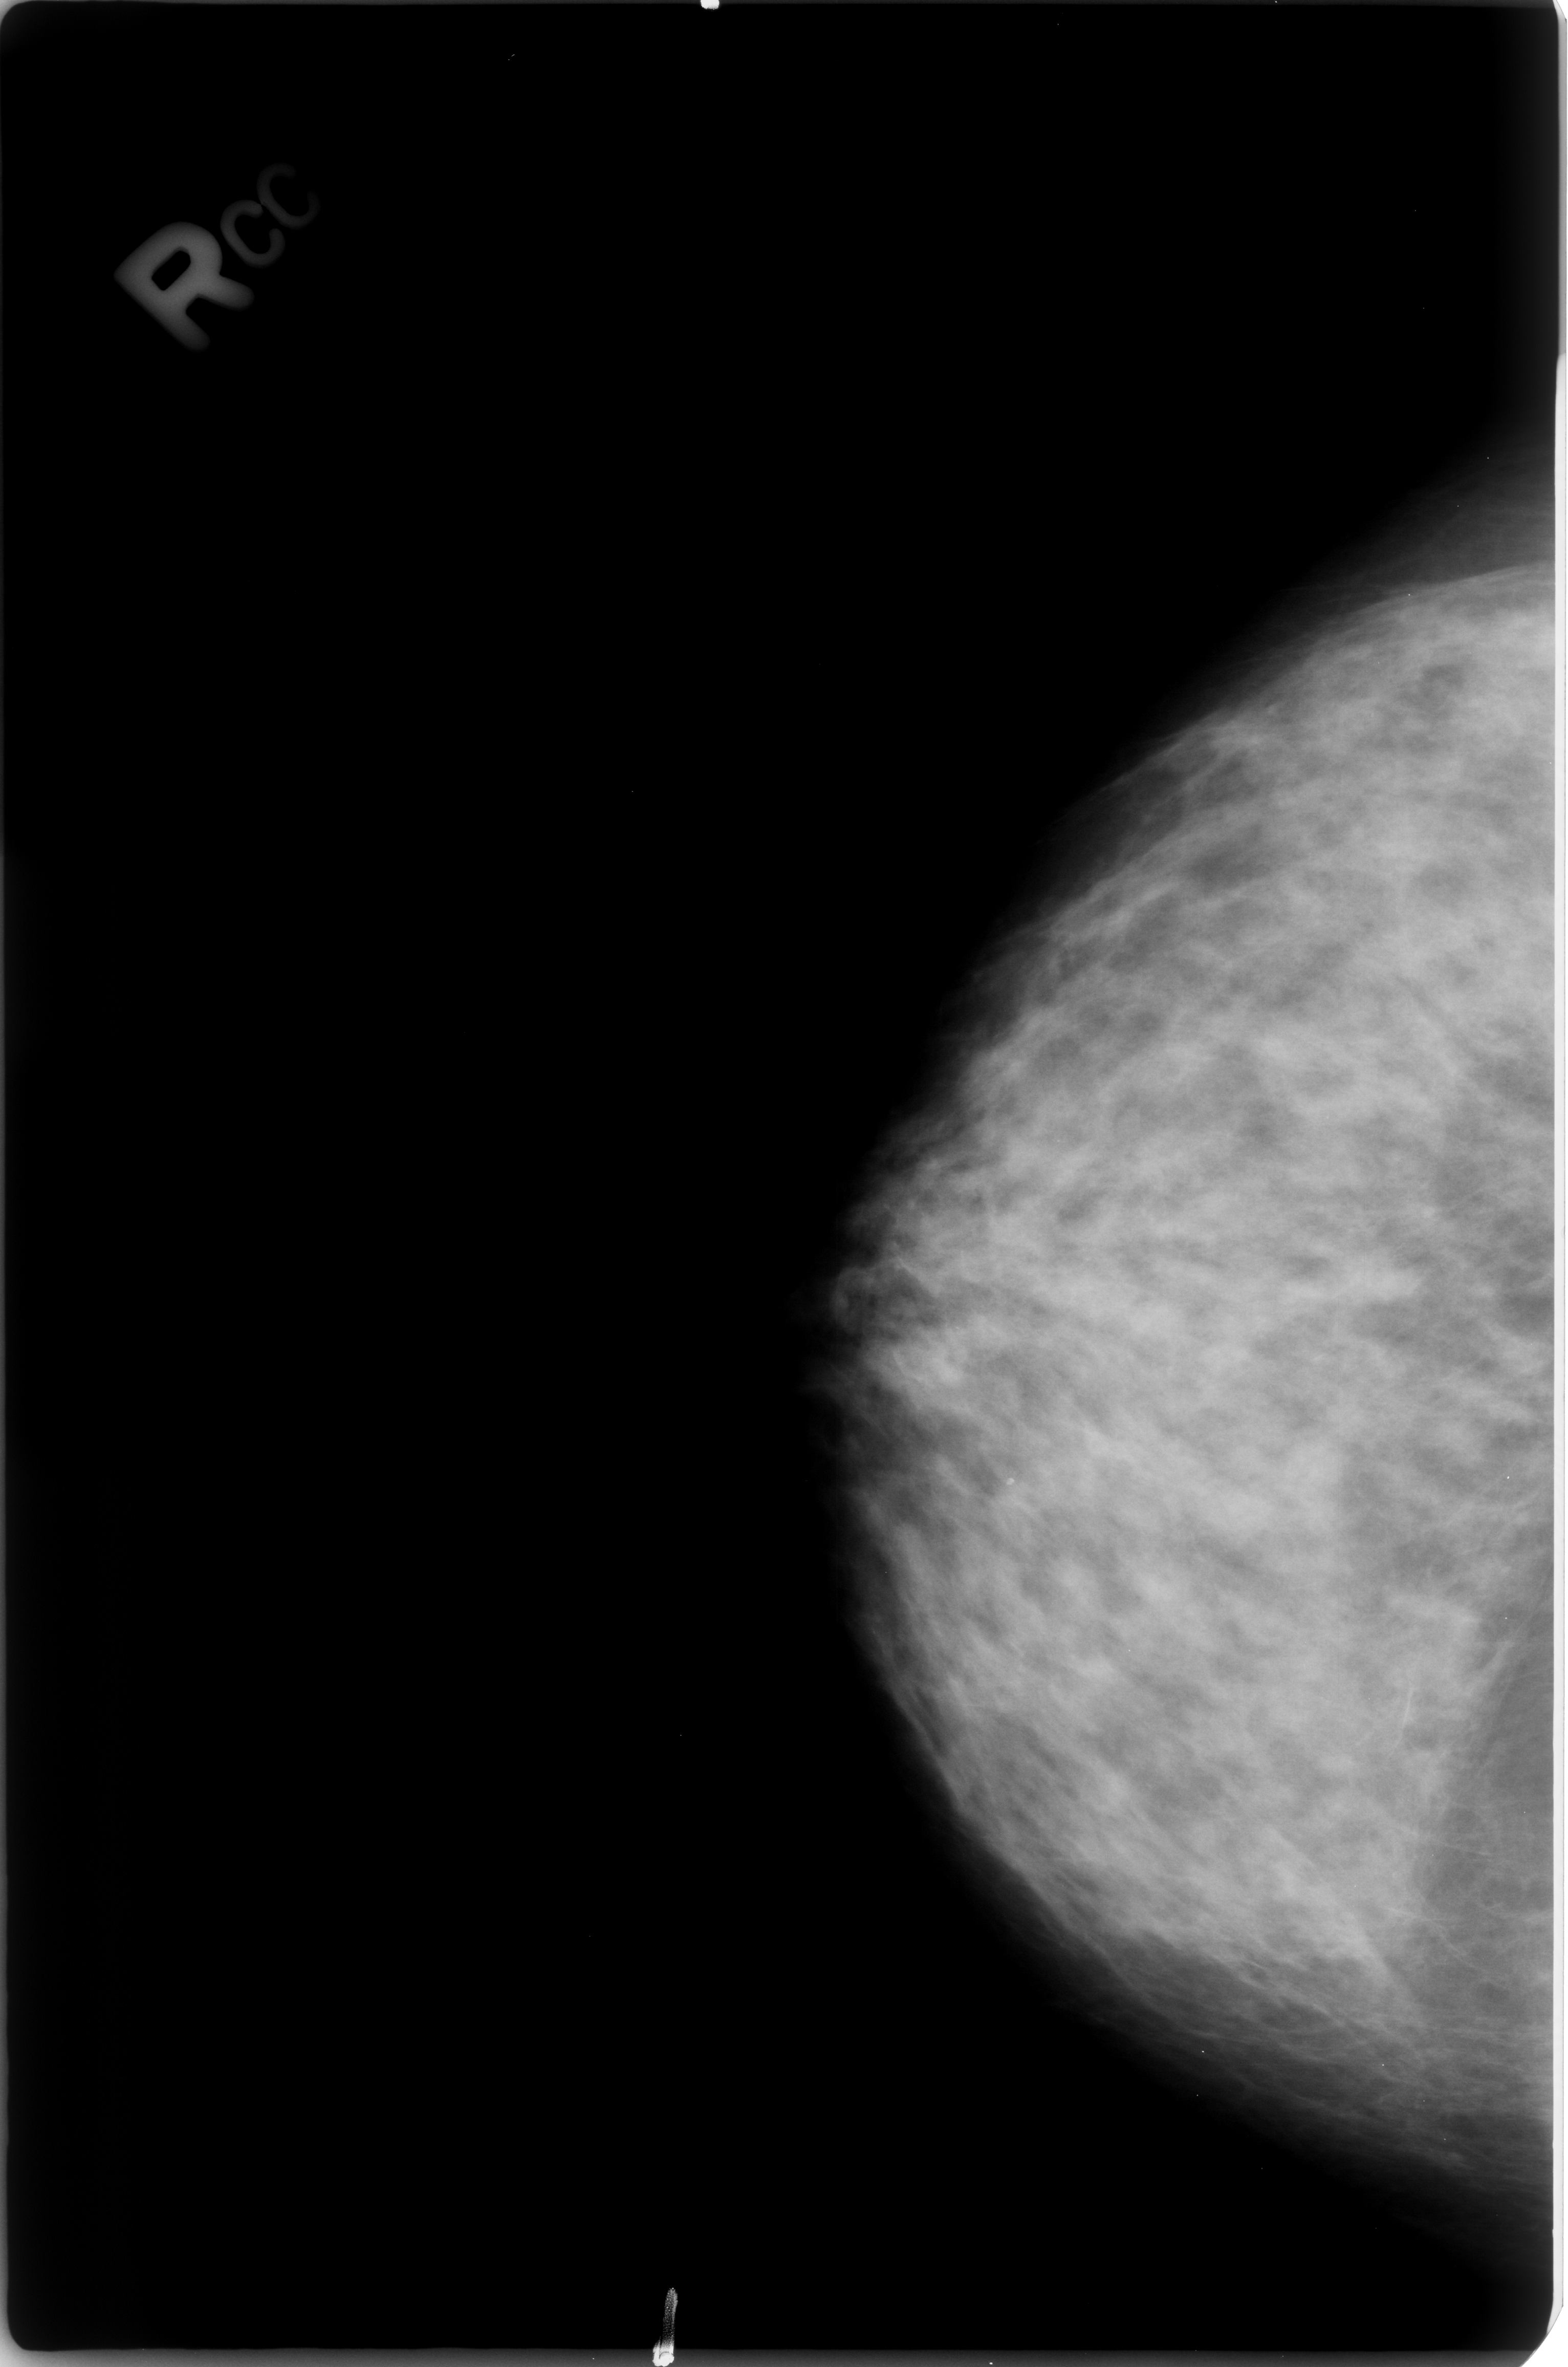
Mammogram (digitized film). Right breast. CC view. 1568 × 2367 image matrix.
Expert-marked regions of interest on this image (one box per marked abnormality):
- calcifications, morphology lucent center; BI-RADS assessment category 2; subtlety rating 3 on a 1 (subtle) to 5 (obvious) scale; benign; no additional work-up was recommended (outcome (as recorded, no biopsy): benign without callback): bounding box (x1, y1, x2, y2) in pixels: (990, 1470, 1025, 1504)